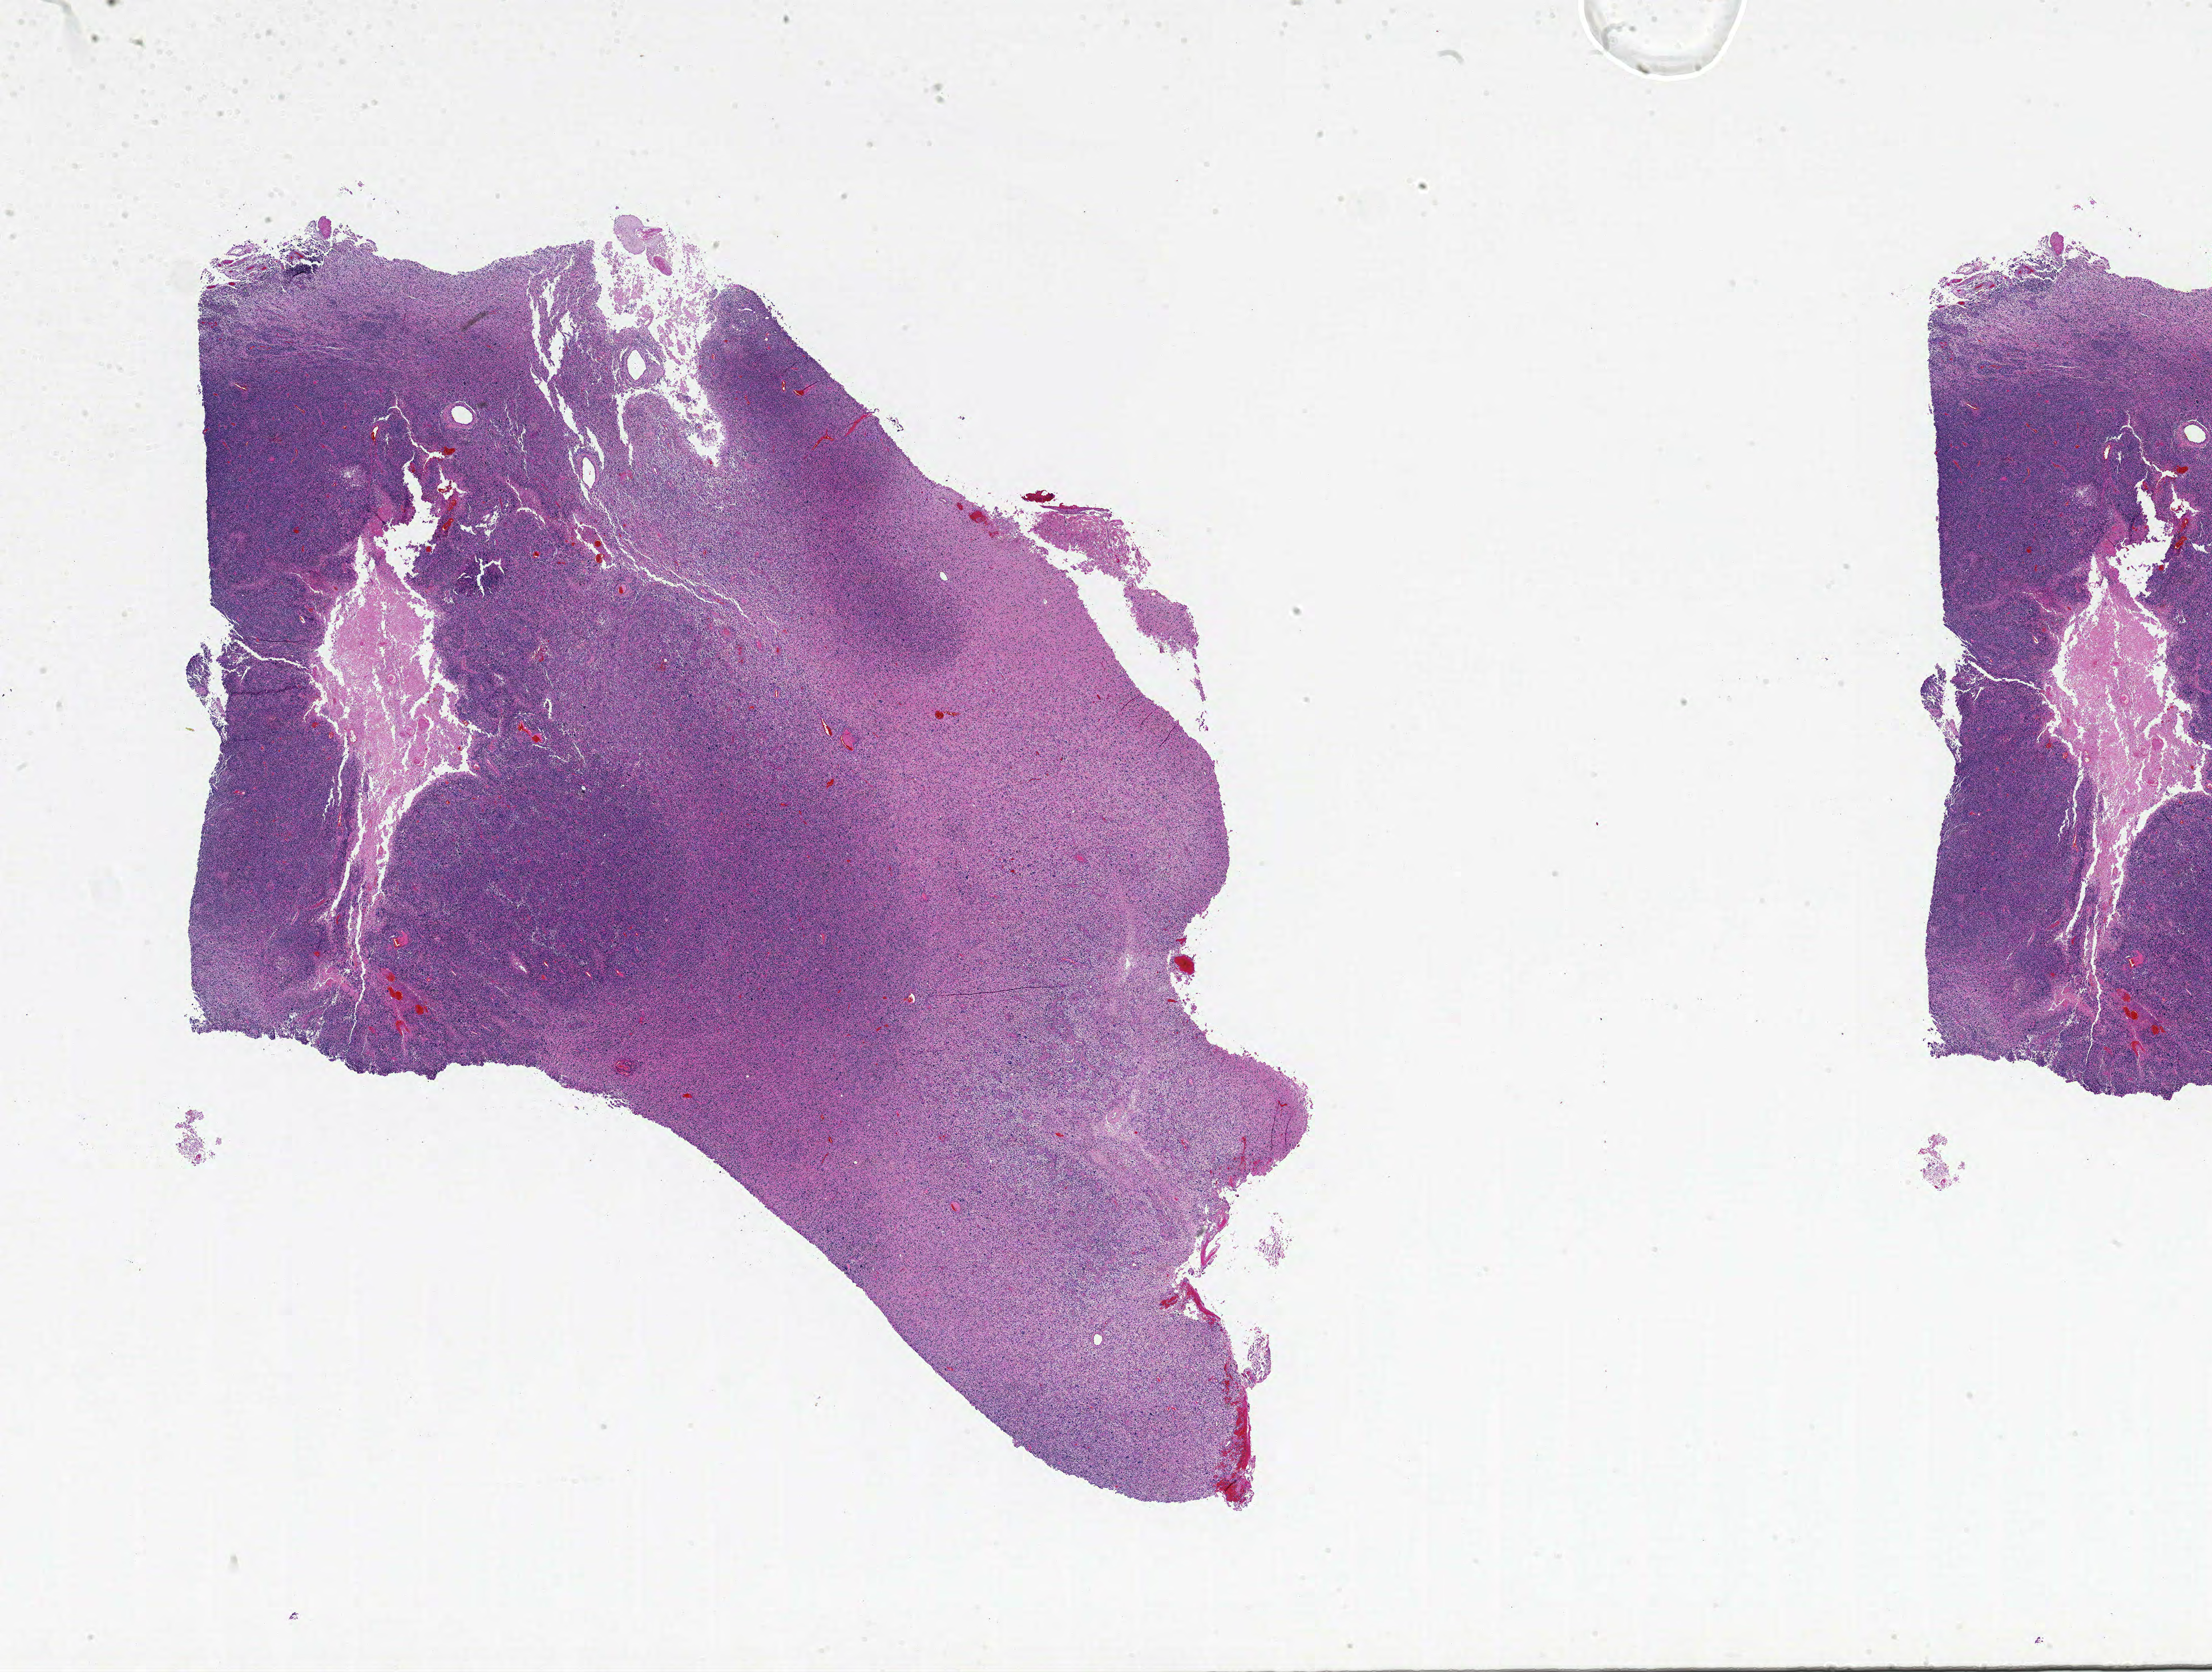
Digitized H&E-stained tissue section (whole slide), a low-resolution overview of the entire scanned area, about 31.0 x 23.4 mm; formalin-fixed paraffin-embedded (FFPE) diagnostic section; sample: primary tumour, brain. Patient: female, age at initial diagnosis 75 years.
Histologic diagnosis: Glioblastoma.